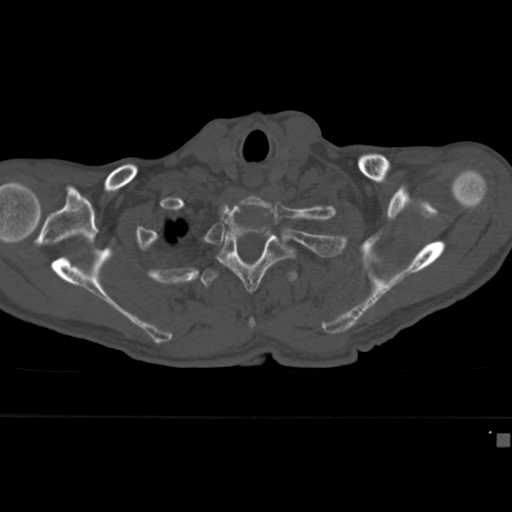
CT including the spine, one axial slice; slice 344 of 430 in the series (ordered by position); reconstruction kernel Br40s; 120 kVp; bone window (W 1800 / L 400 HU); 1.5 mm slice thickness; 512 × 512 image matrix. Male patient, age 64 years. Case-level facts recorded for this patient, not image findings: primary cancer: uterus.
Annotated regions visible in this slice (semi-automatic segmentation, software-assisted and operator-edited):
- T2 vertebra: bounding box (x1, y1, x2, y2) in pixels: (216, 231, 296, 292)
- T3 vertebra: (200, 269, 298, 330)